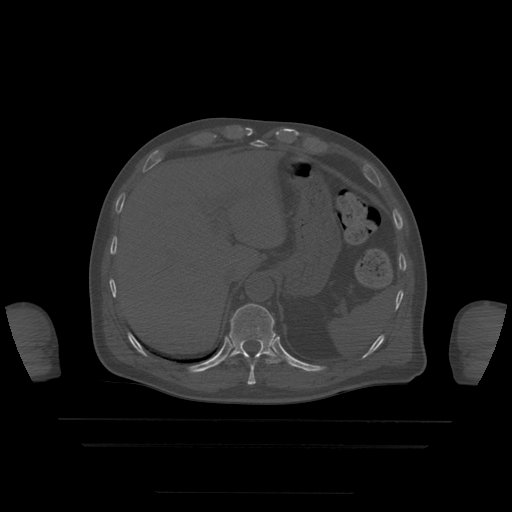
CT including the spine, one axial slice; slice 227 of 522 in the series (ordered by position); bone window (W 1800 / L 400 HU); 512 × 512 image matrix, field of view 436 × 436 mm. Patient age 68 years. Case-level facts recorded for this patient, not image findings: primary cancer: urothelial.
Structures marked on this image (semi-automatically segmented with operator editing):
- T10 vertebra: bounding box <247,358,272,385> (left, top, right, bottom; pixels)
- T11 vertebra: <224,304,283,364>